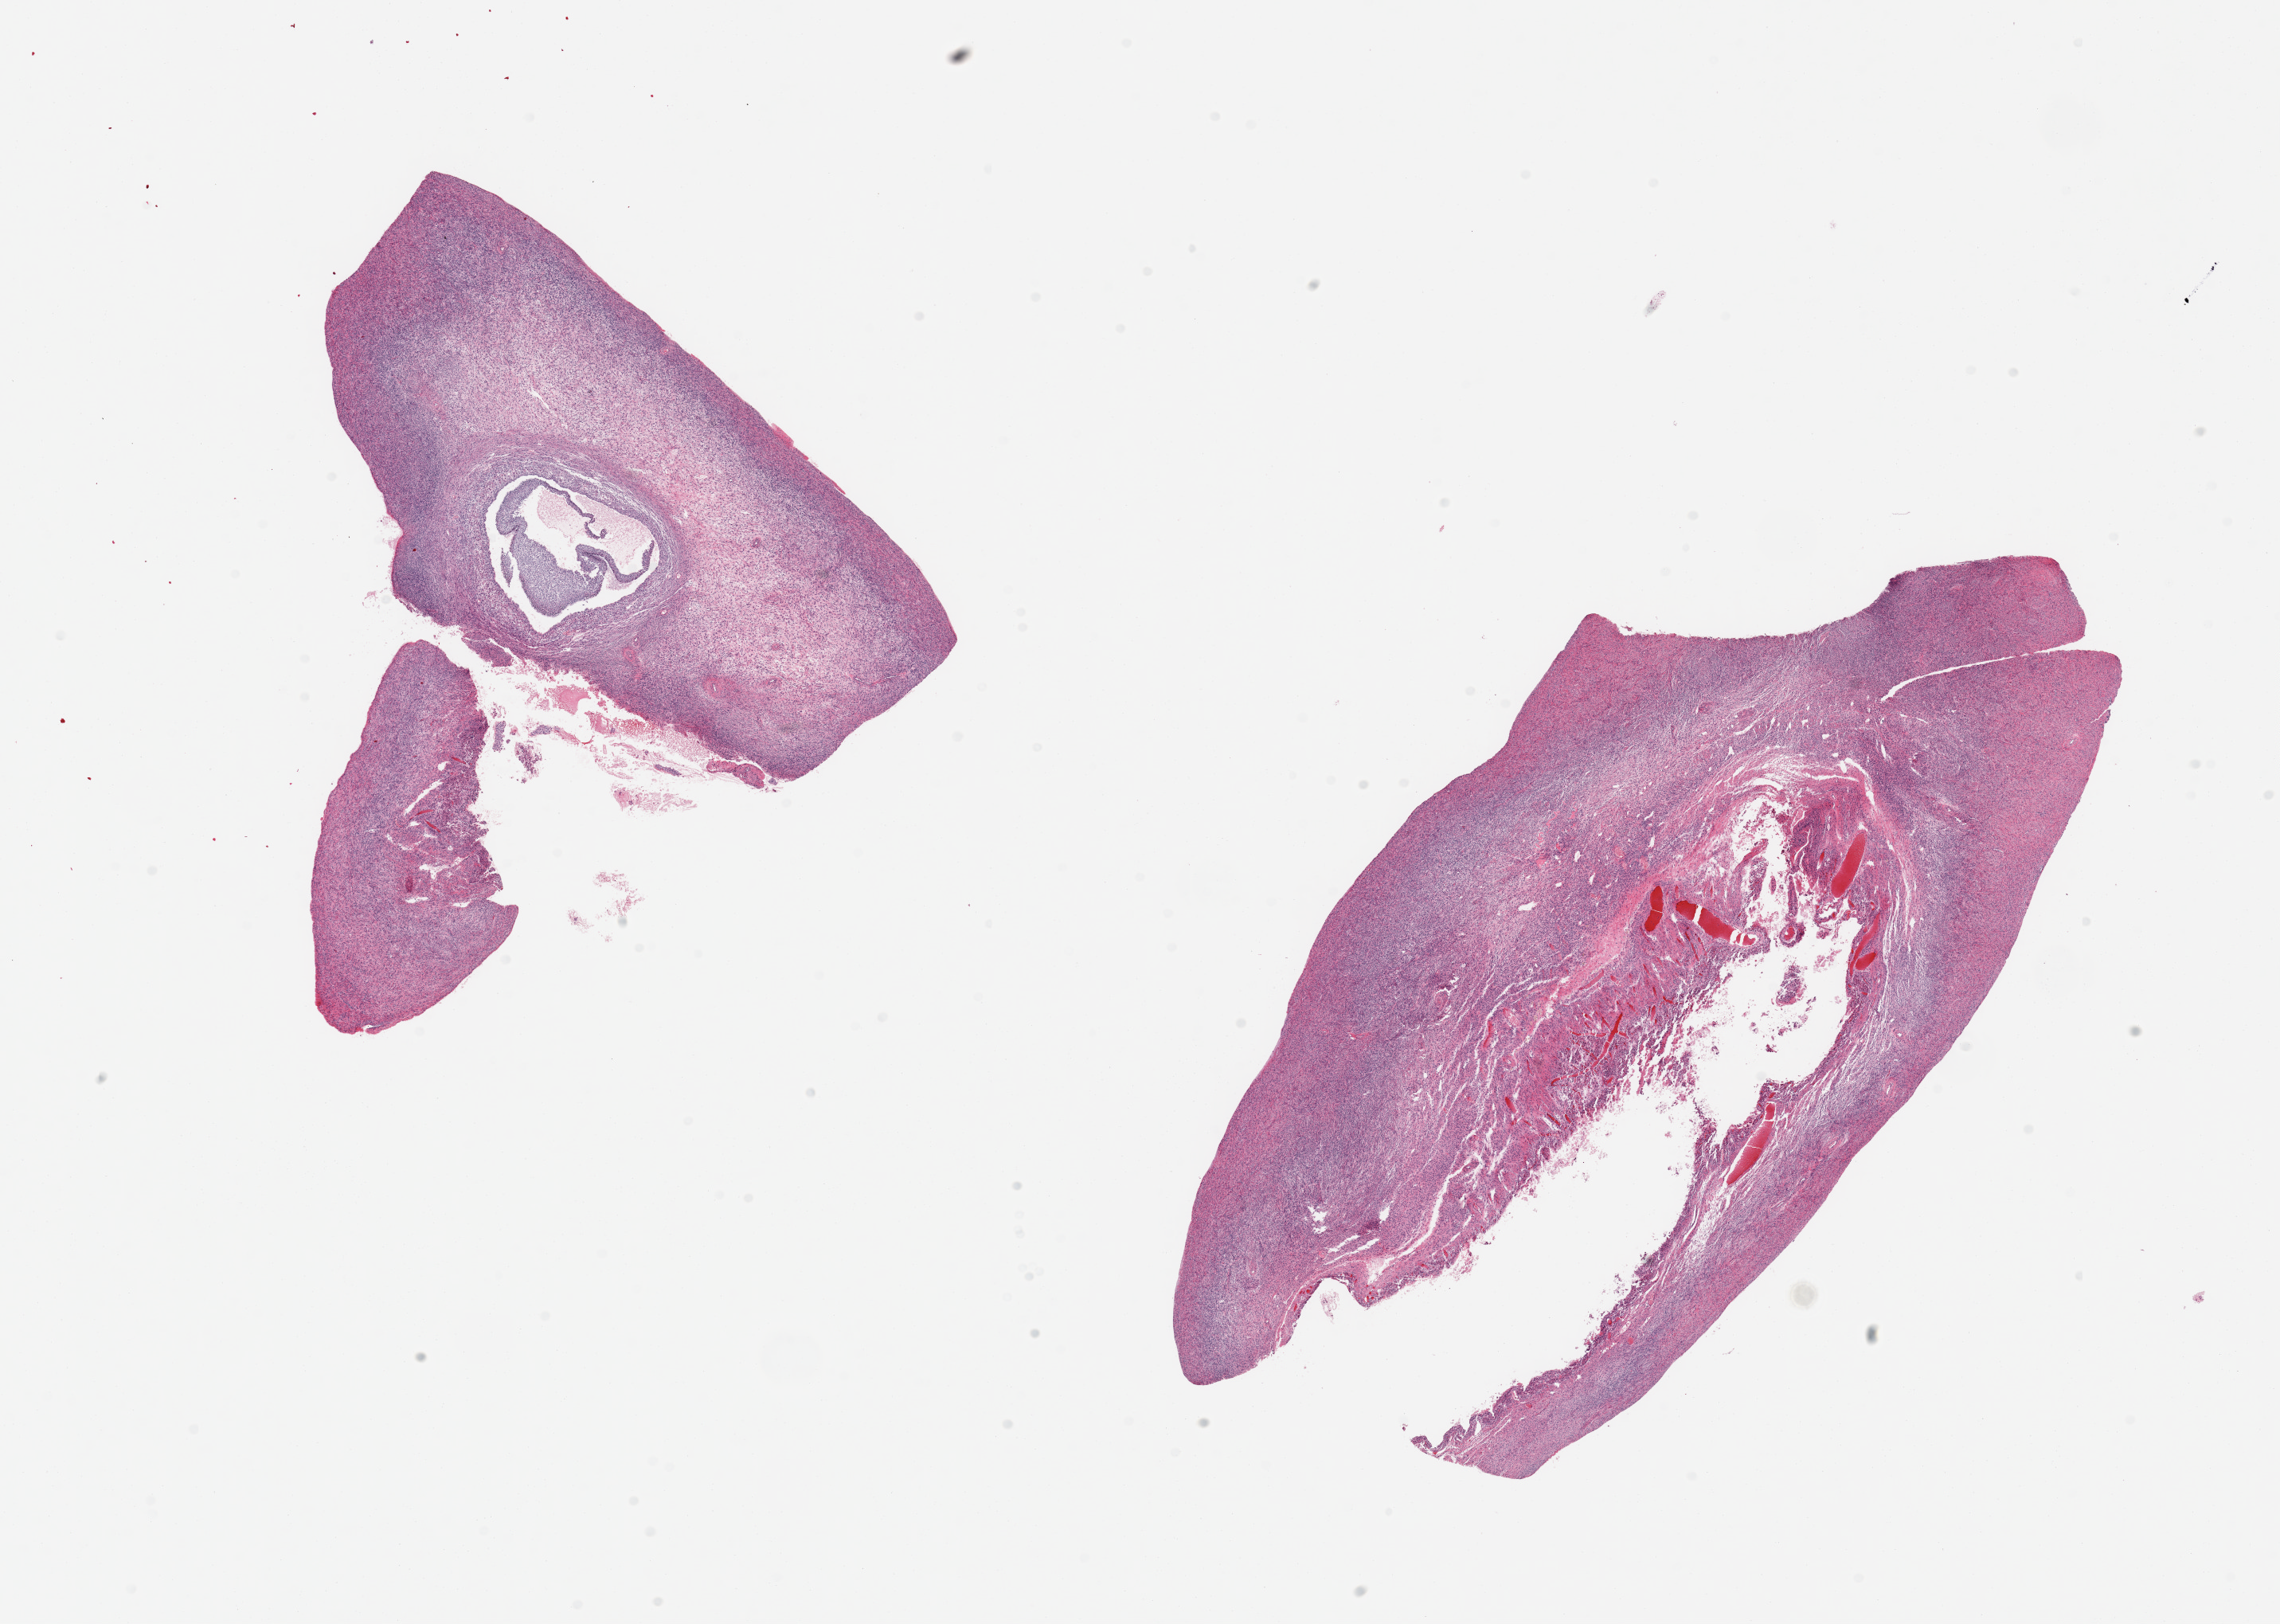
Whole-slide image, hematoxylin and eosin (H&E) stain — shown as a low-resolution overview of the whole scanned area (about 22.6 x 16.1 mm); PAXgene-fixed paraffin-embedded (PFPE) section; sampled site (target tissue): ovary; donor tissue sample. Donor sex: female.
* pathologist's review note for this sample: 2 pieces; graffian and corpus luteum cysts